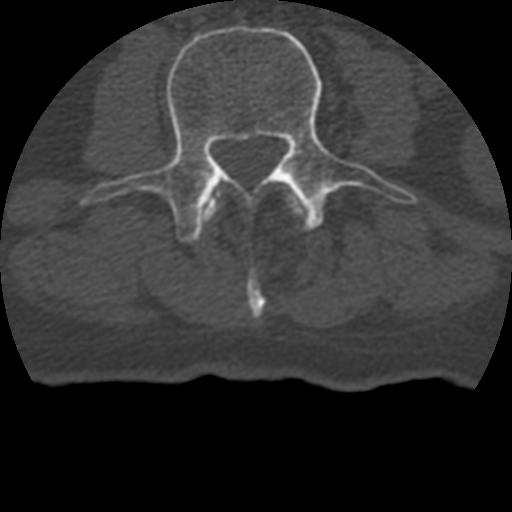
CT including the spine, one axial slice; slice 95 of 399 in the series (ordered by position); reconstruction kernel STANDARD; 120 kVp; bone window (W 1800 / L 400 HU); 1.25 mm slice thickness; 512 × 512 image matrix, field of view 160 × 160 mm. Patient age 69 years. From the clinical record (not read from this slice): primary cancer: prostate.
Structures marked on this image (semi-automatic segmentation, software-assisted and operator-edited):
- L2 vertebra: bounding box <205,197,304,317> (left, top, right, bottom; pixels)
- L3 vertebra: <77,25,412,242>